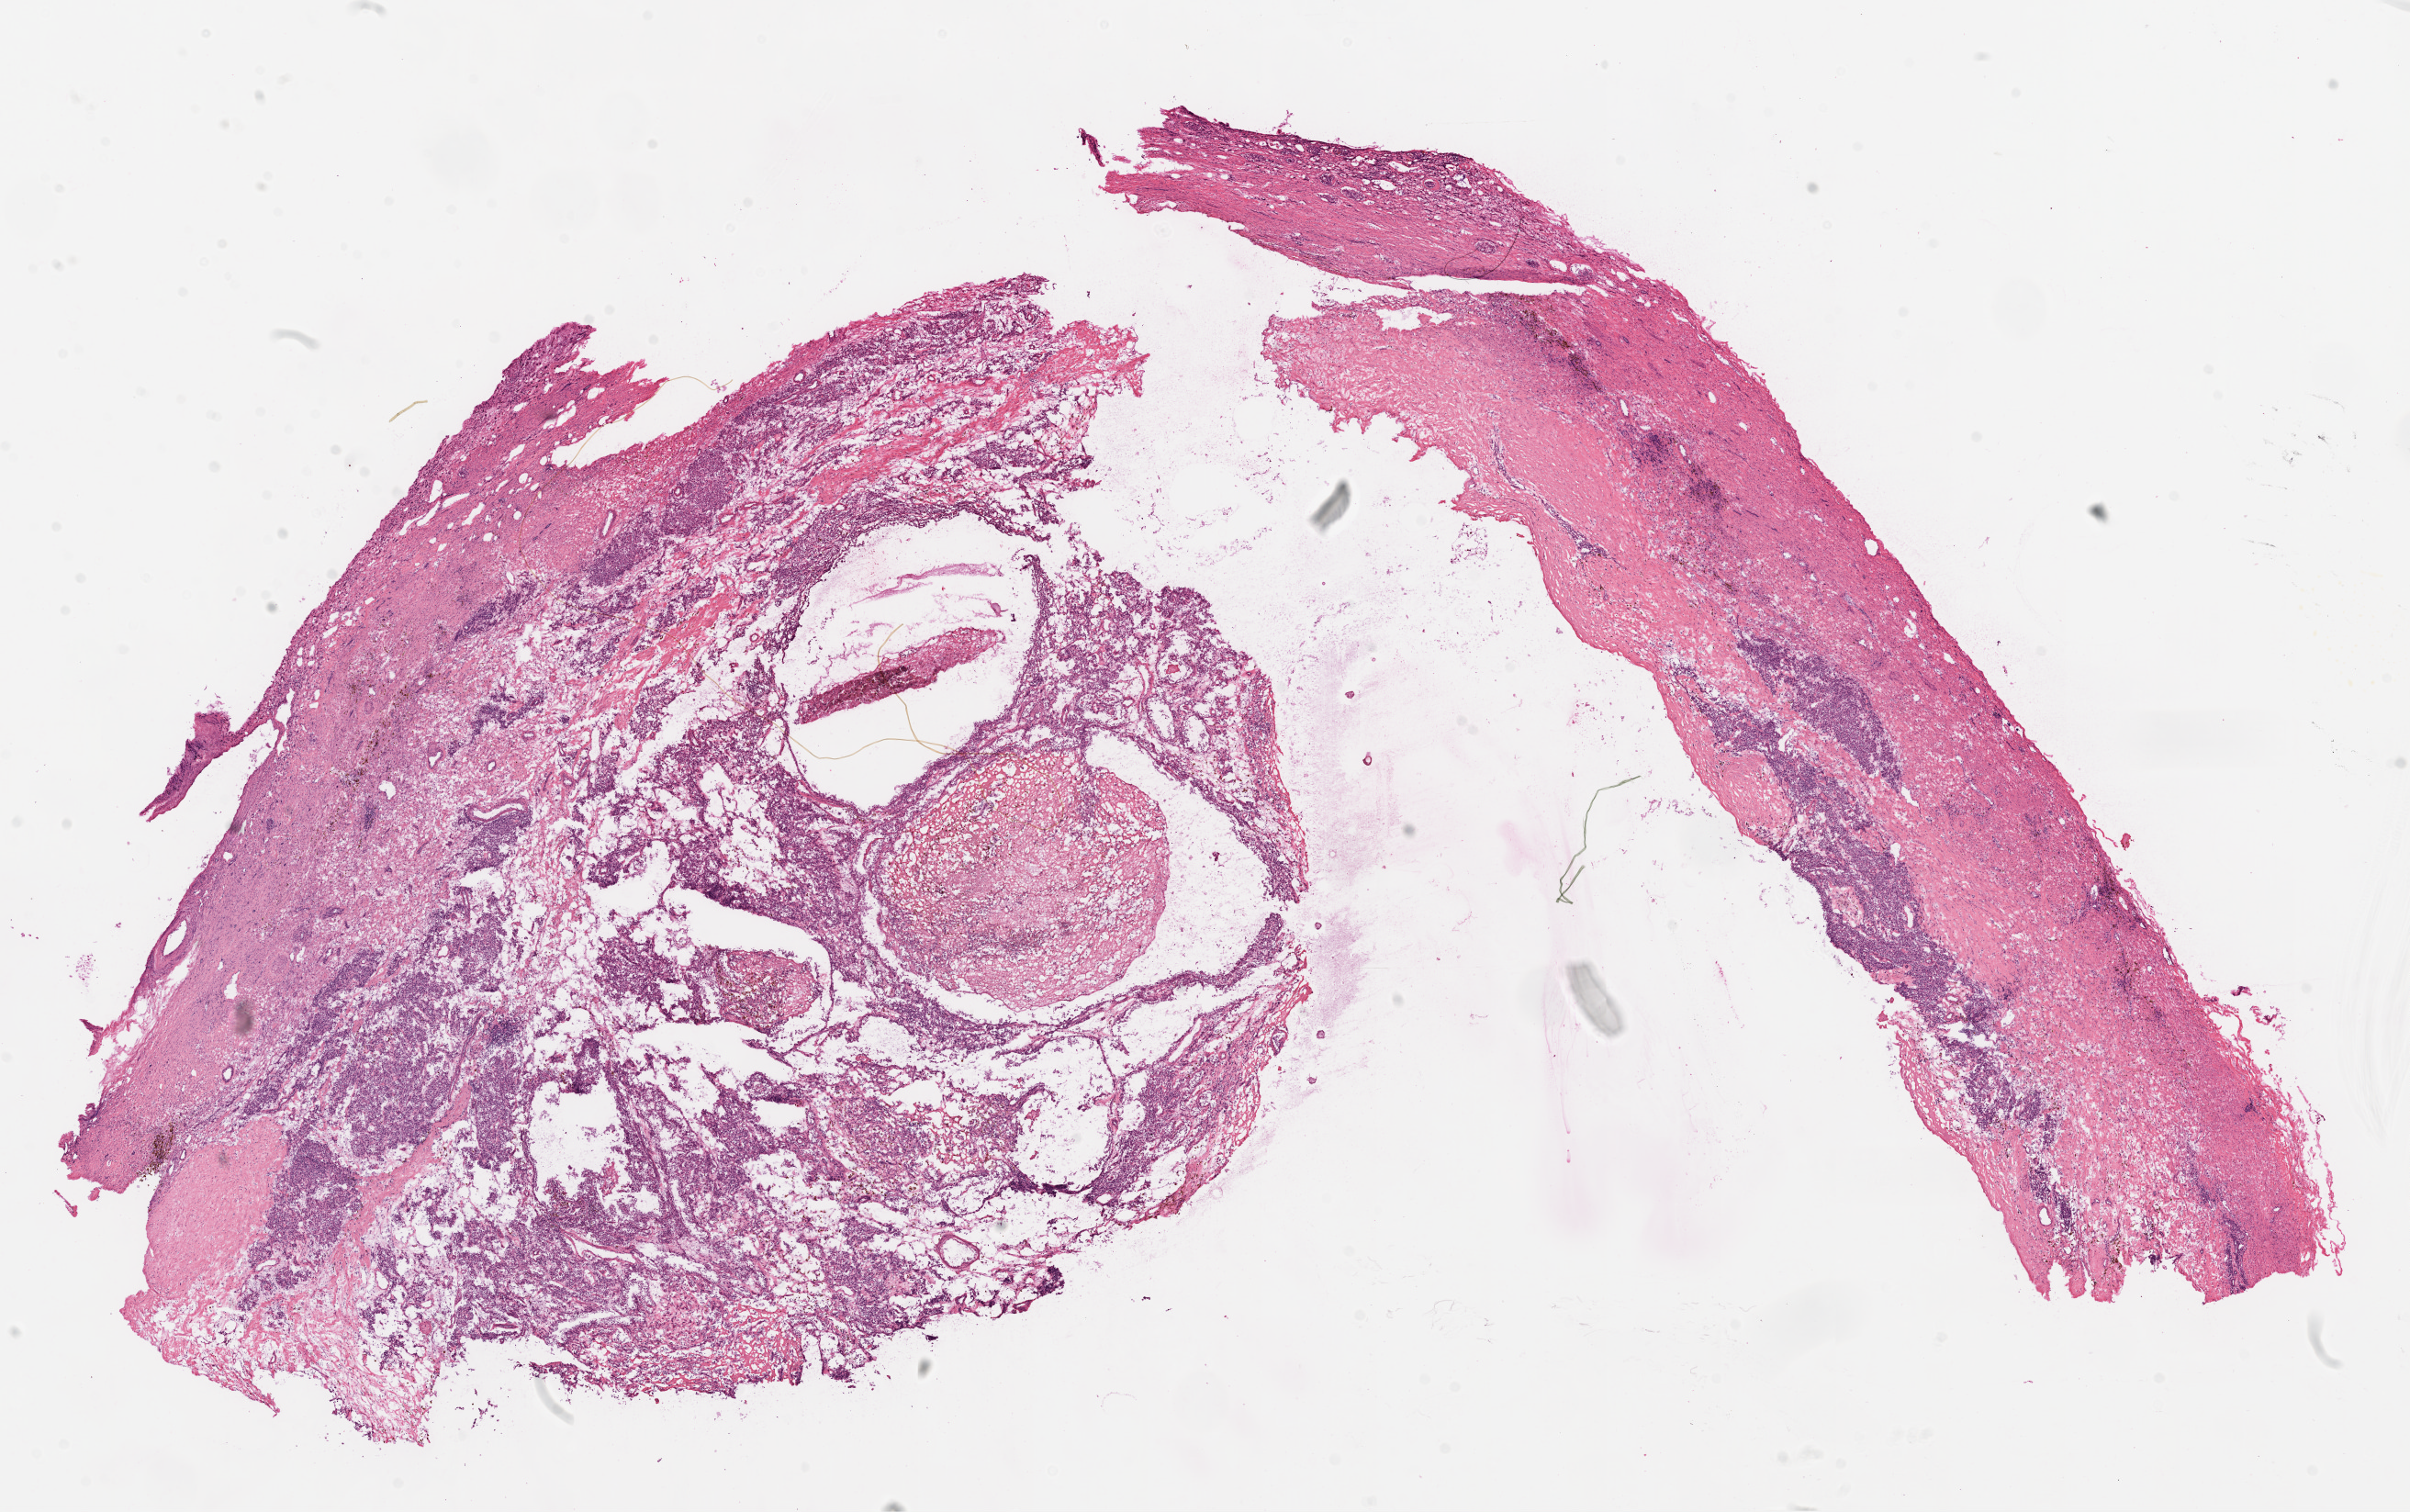
H&E-stained whole-slide image, whole scanned area (about 21.1 x 13.2 mm) shown as a low-resolution overview; frozen section; primary tumour sample from the kidney. Male patient; age at initial diagnosis 37 years.
Histologic diagnosis: Clear cell adenocarcinoma, NOS.